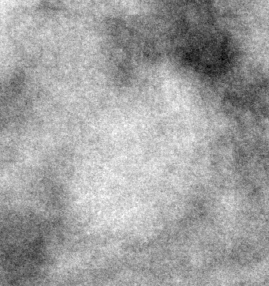
Region of interest cut from a scanned film mammogram (one marked finding), right breast, MLO view, BI-RADS breast density category 4 (scale 1–4).
Finding: mass, shape oval, margins circumscribed; BI-RADS assessment category 3; benign without callback (not worked up further).